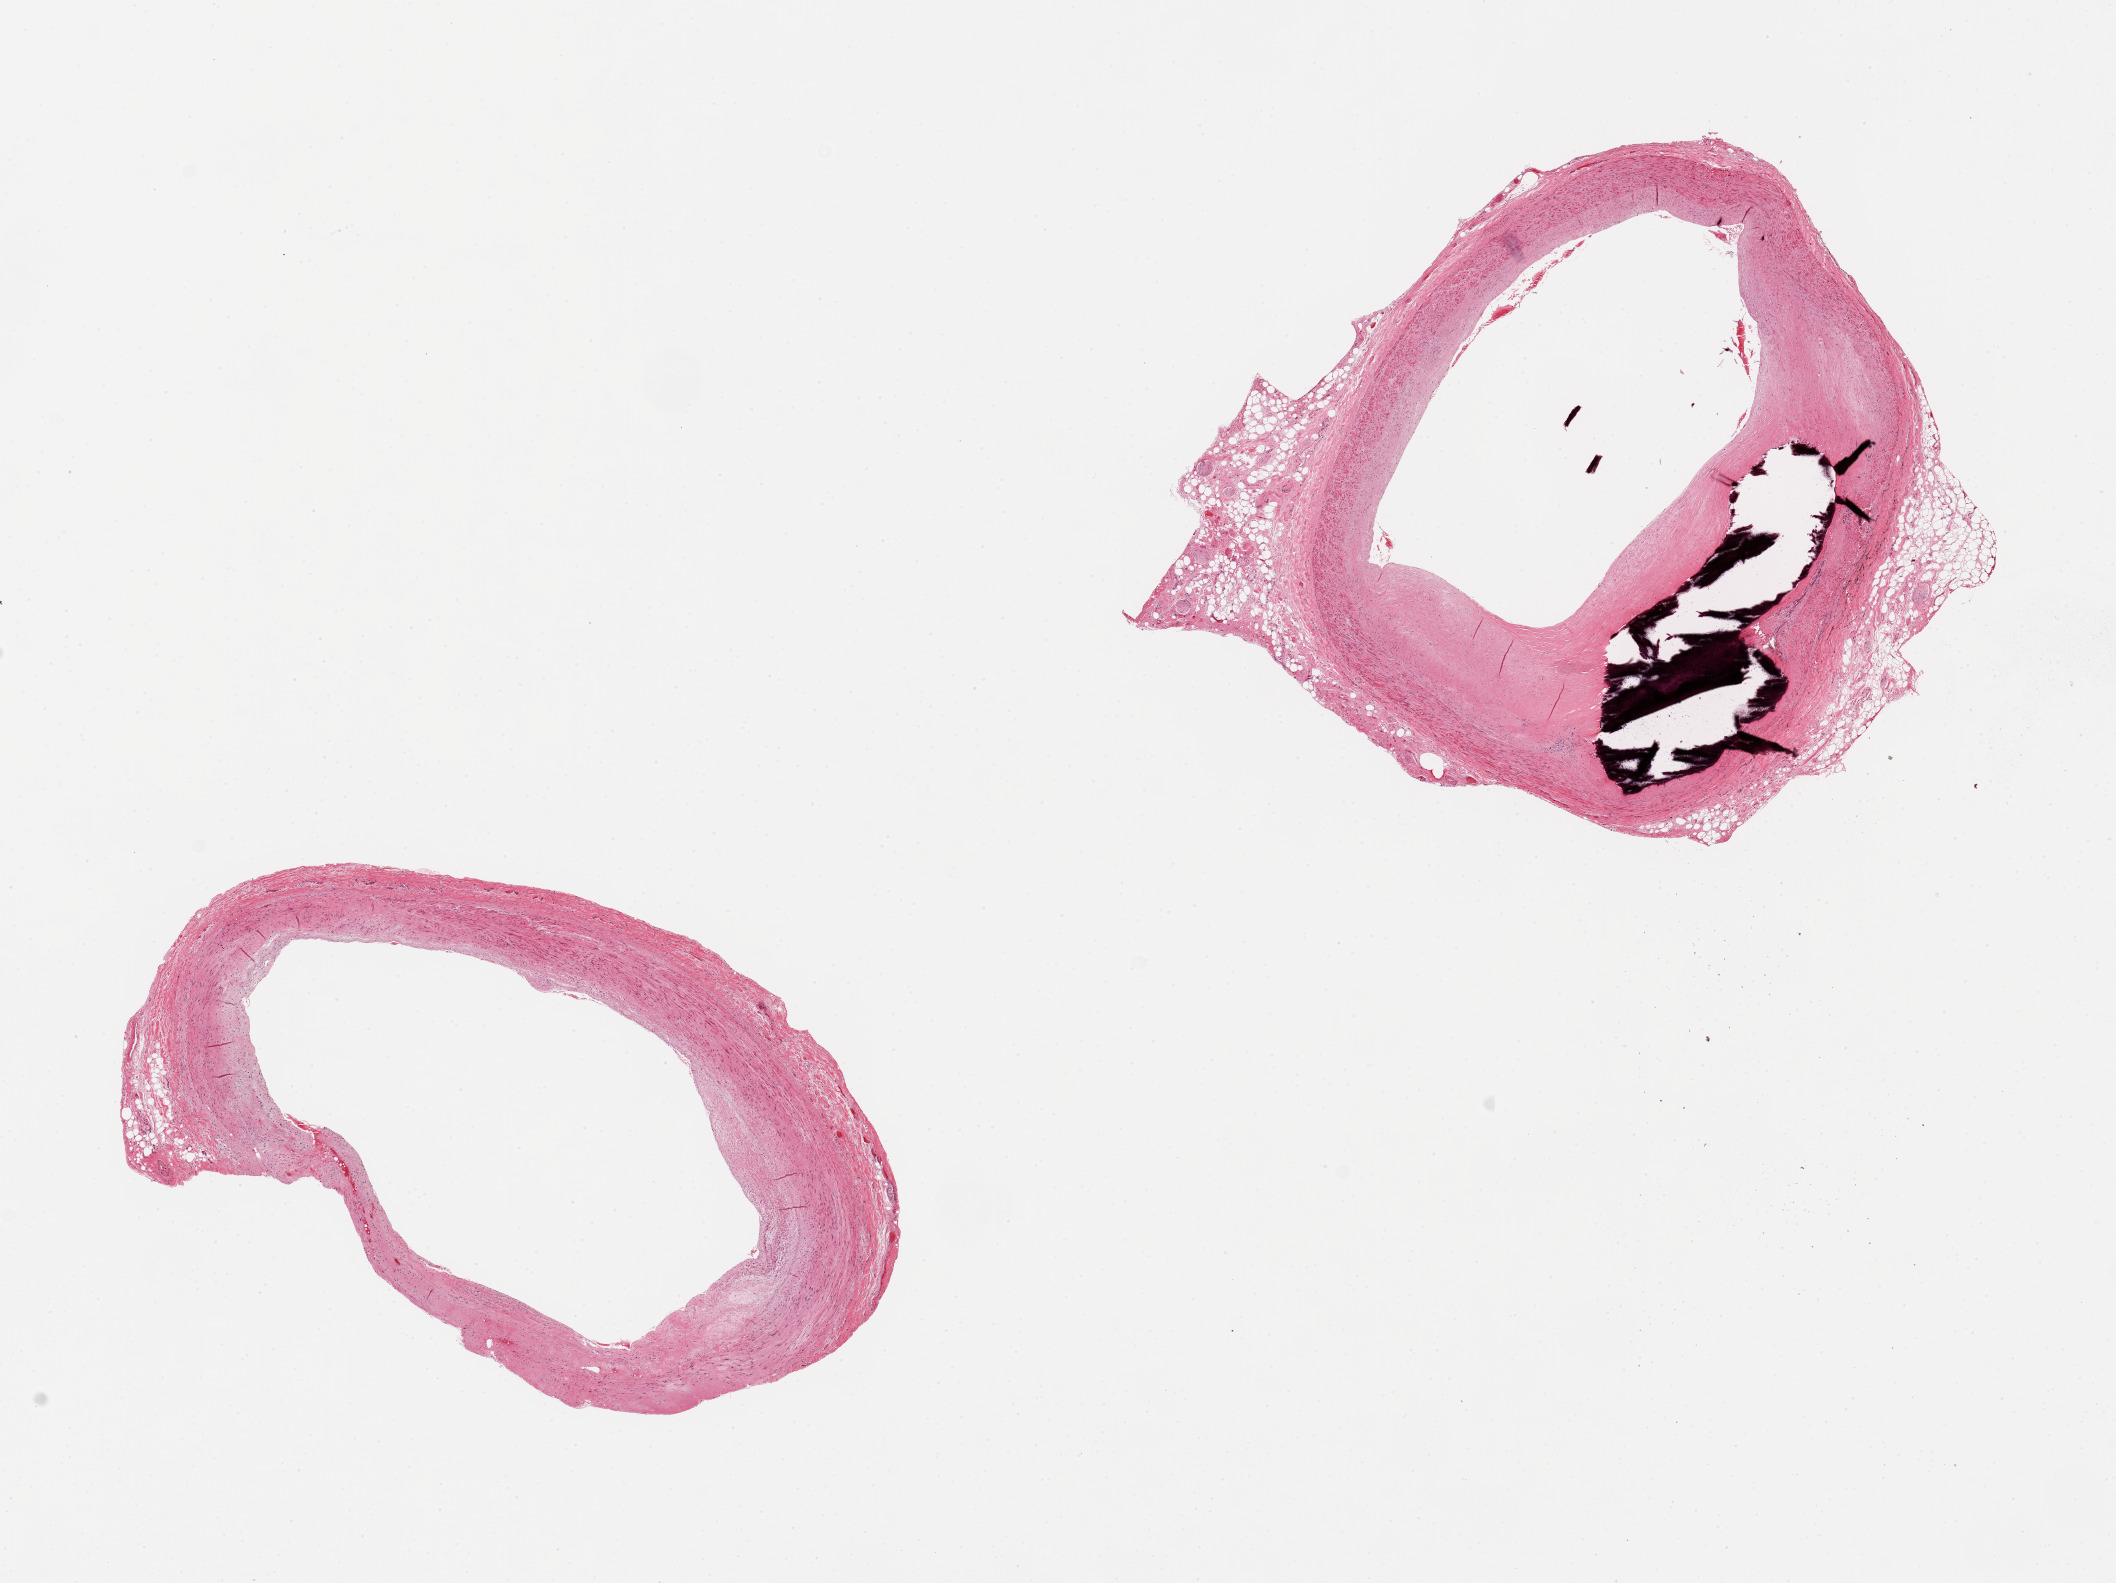
Whole-slide image, H&E stain, low-resolution overview of the scanned area, about 16.7 x 12.5 mm; PAXgene-fixed, paraffin-embedded tissue; section of coronary artery (target tissue); donor tissue sample. Donor: male.
Pathologist's review note for this sample: 2 pieces; calcific atherosclerosis with up to 50% narrowing of the lumen, attached fat and nerve up to 20% of one piece.